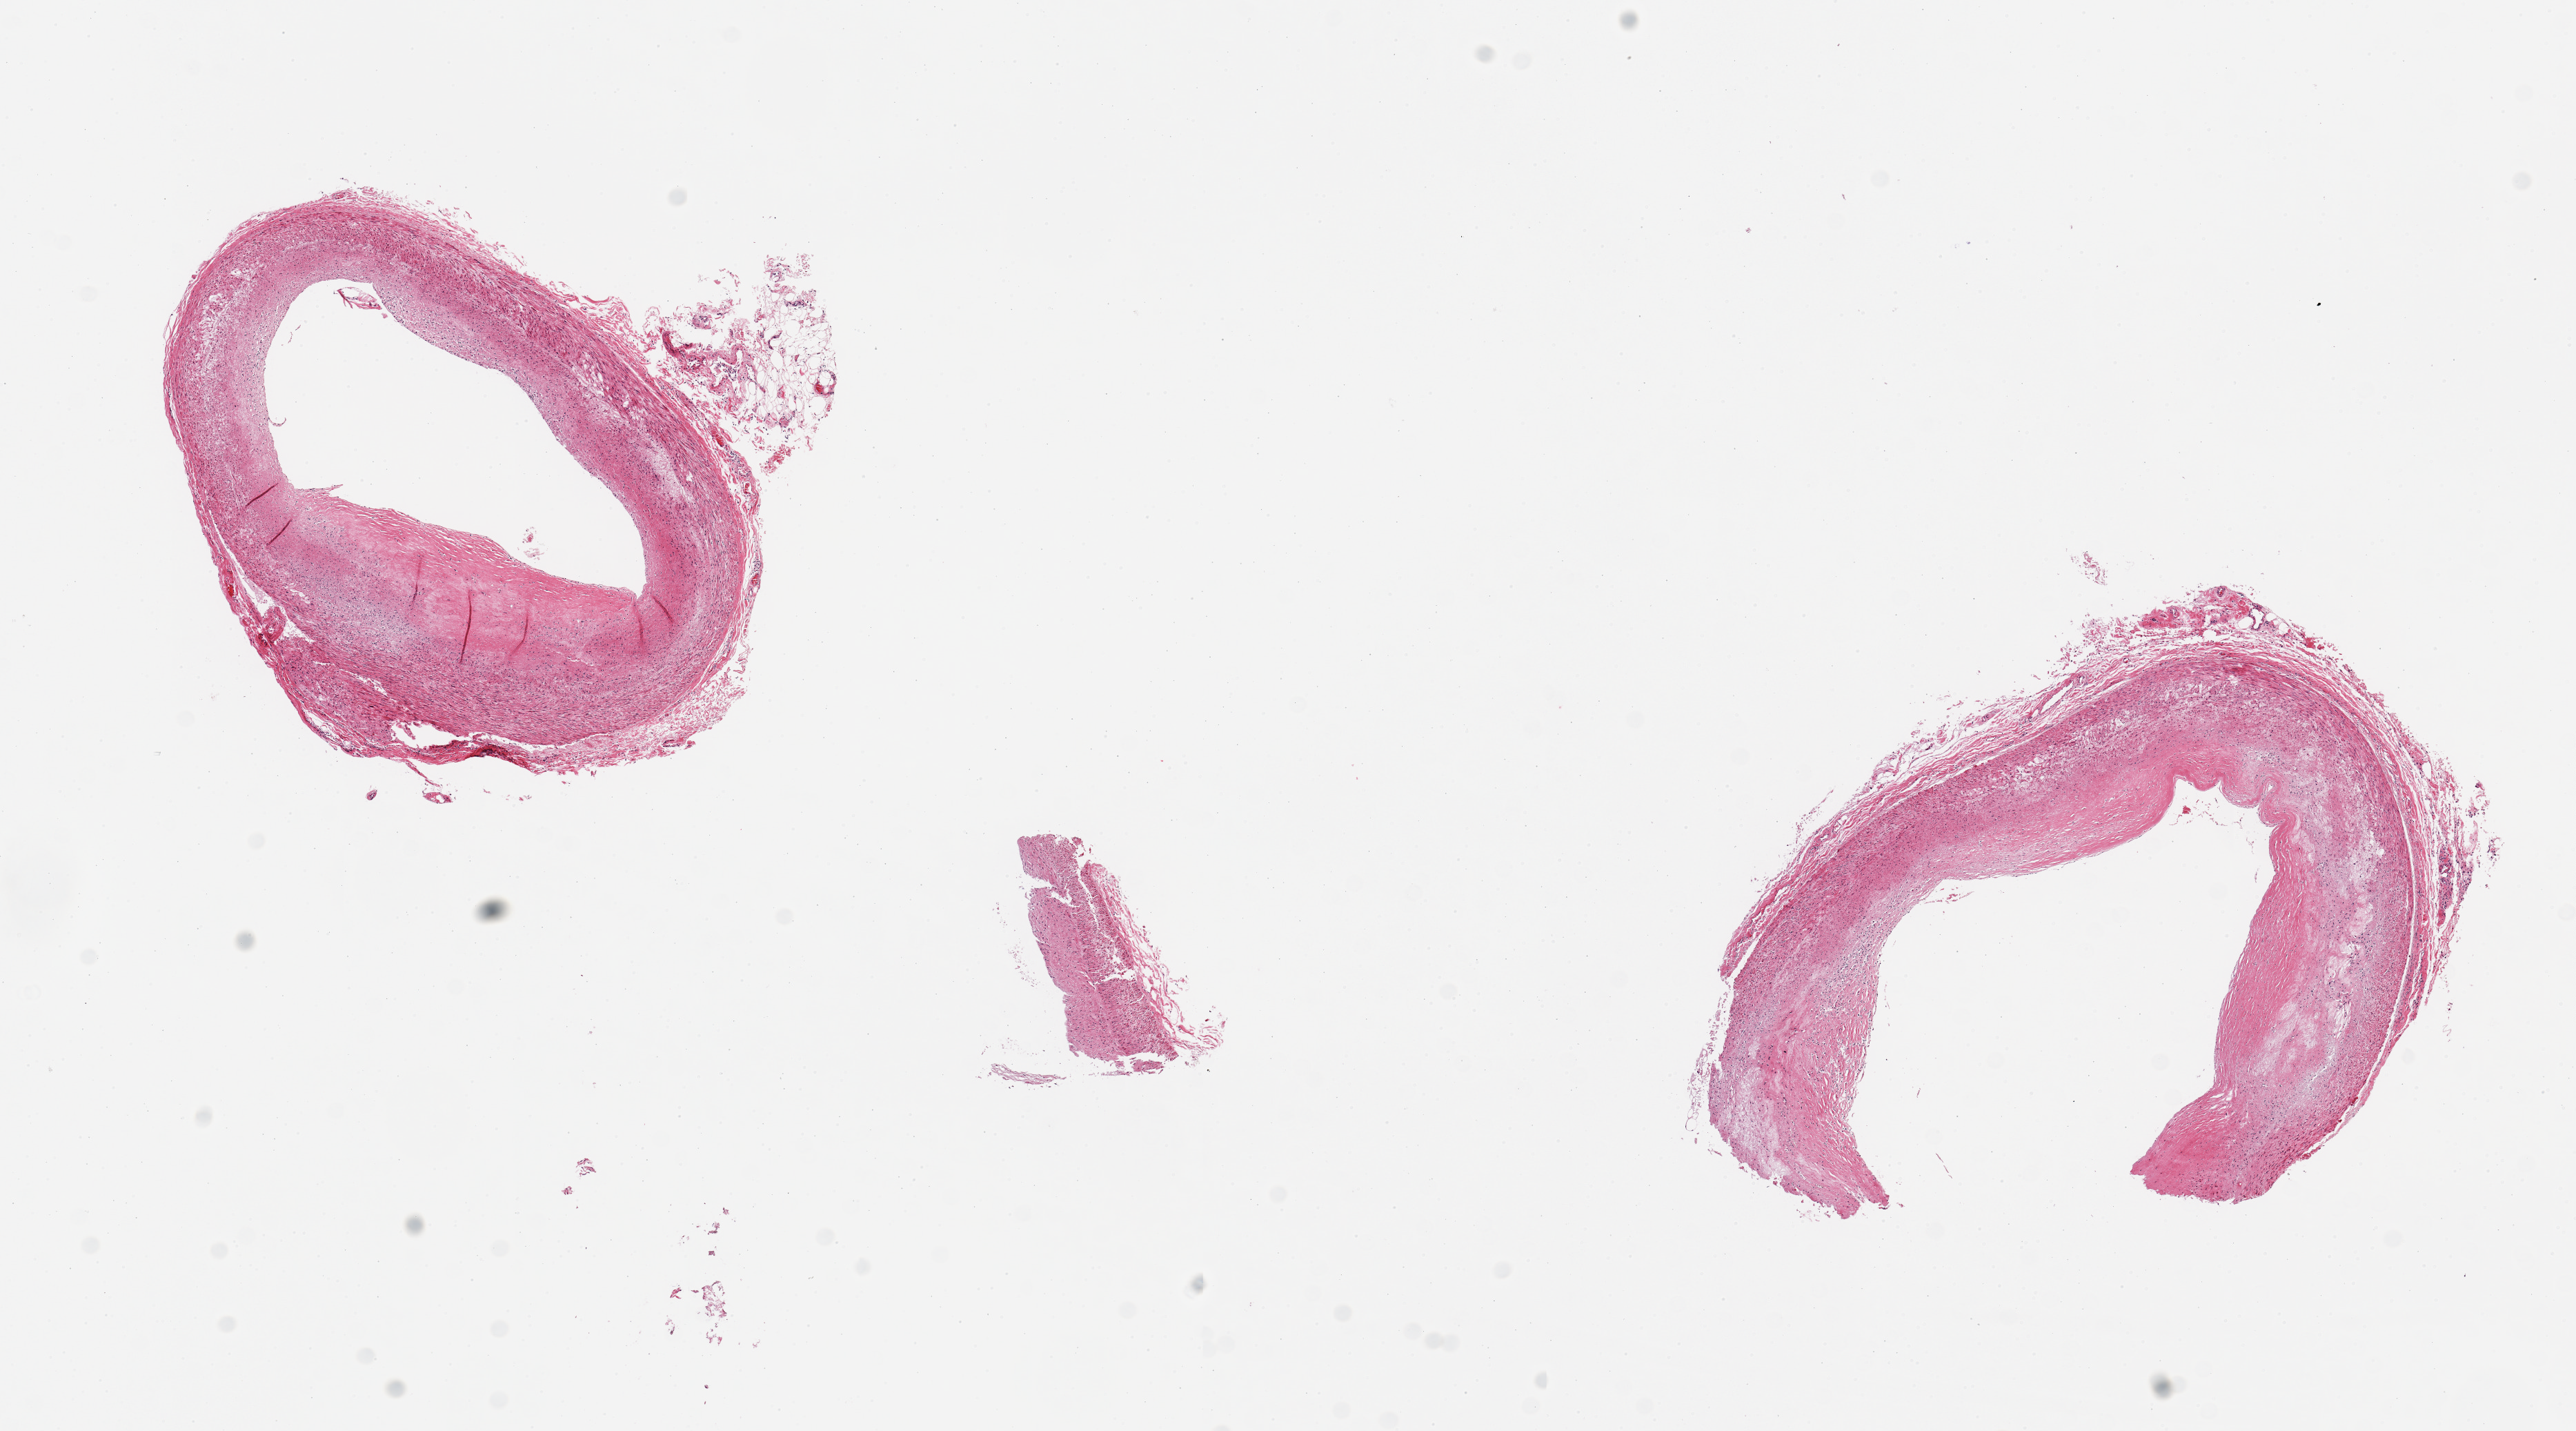
H&E whole-slide image, whole scanned area (about 14.8 x 8.2 mm, from a 20x scan) shown as a low-resolution overview, PAXgene-fixed paraffin-embedded (PFPE) section, sampled site (target tissue): coronary artery, donor tissue sample. Donor sex: male.
Review note (as recorded): 2 pieces, moderate atherosis ~30% luminal occlusion.